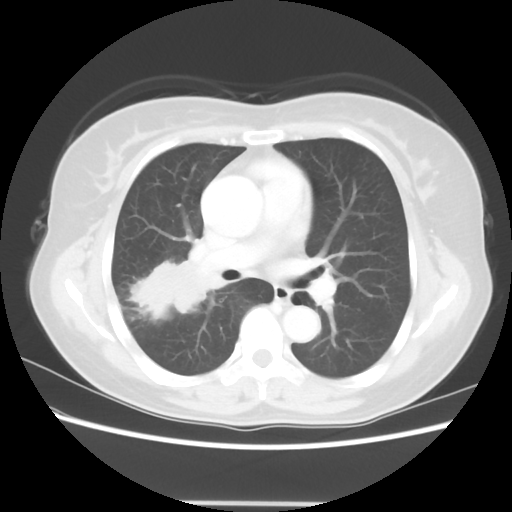
Chest CT, one axial slice. Slice 34 of 56 in the series (ordered by position). Reconstruction kernel STANDARD. 120 kVp. Lung window (W 1500 / L -600 HU). 5 mm slice thickness. 512 × 512 image matrix, field of view 360 × 360 mm. Female patient, age 55 years. Case-level facts recorded for this patient, not image findings: clinical TNM (as recorded): T2 N1 M0; histopathological grade: G2-3.
Outlined on this slice (rectangle marked by the reading radiologist):
- lung tumour (recorded histology: adenocarcinoma): bounding box [x1, y1, x2, y2] px = [122, 249, 226, 327]